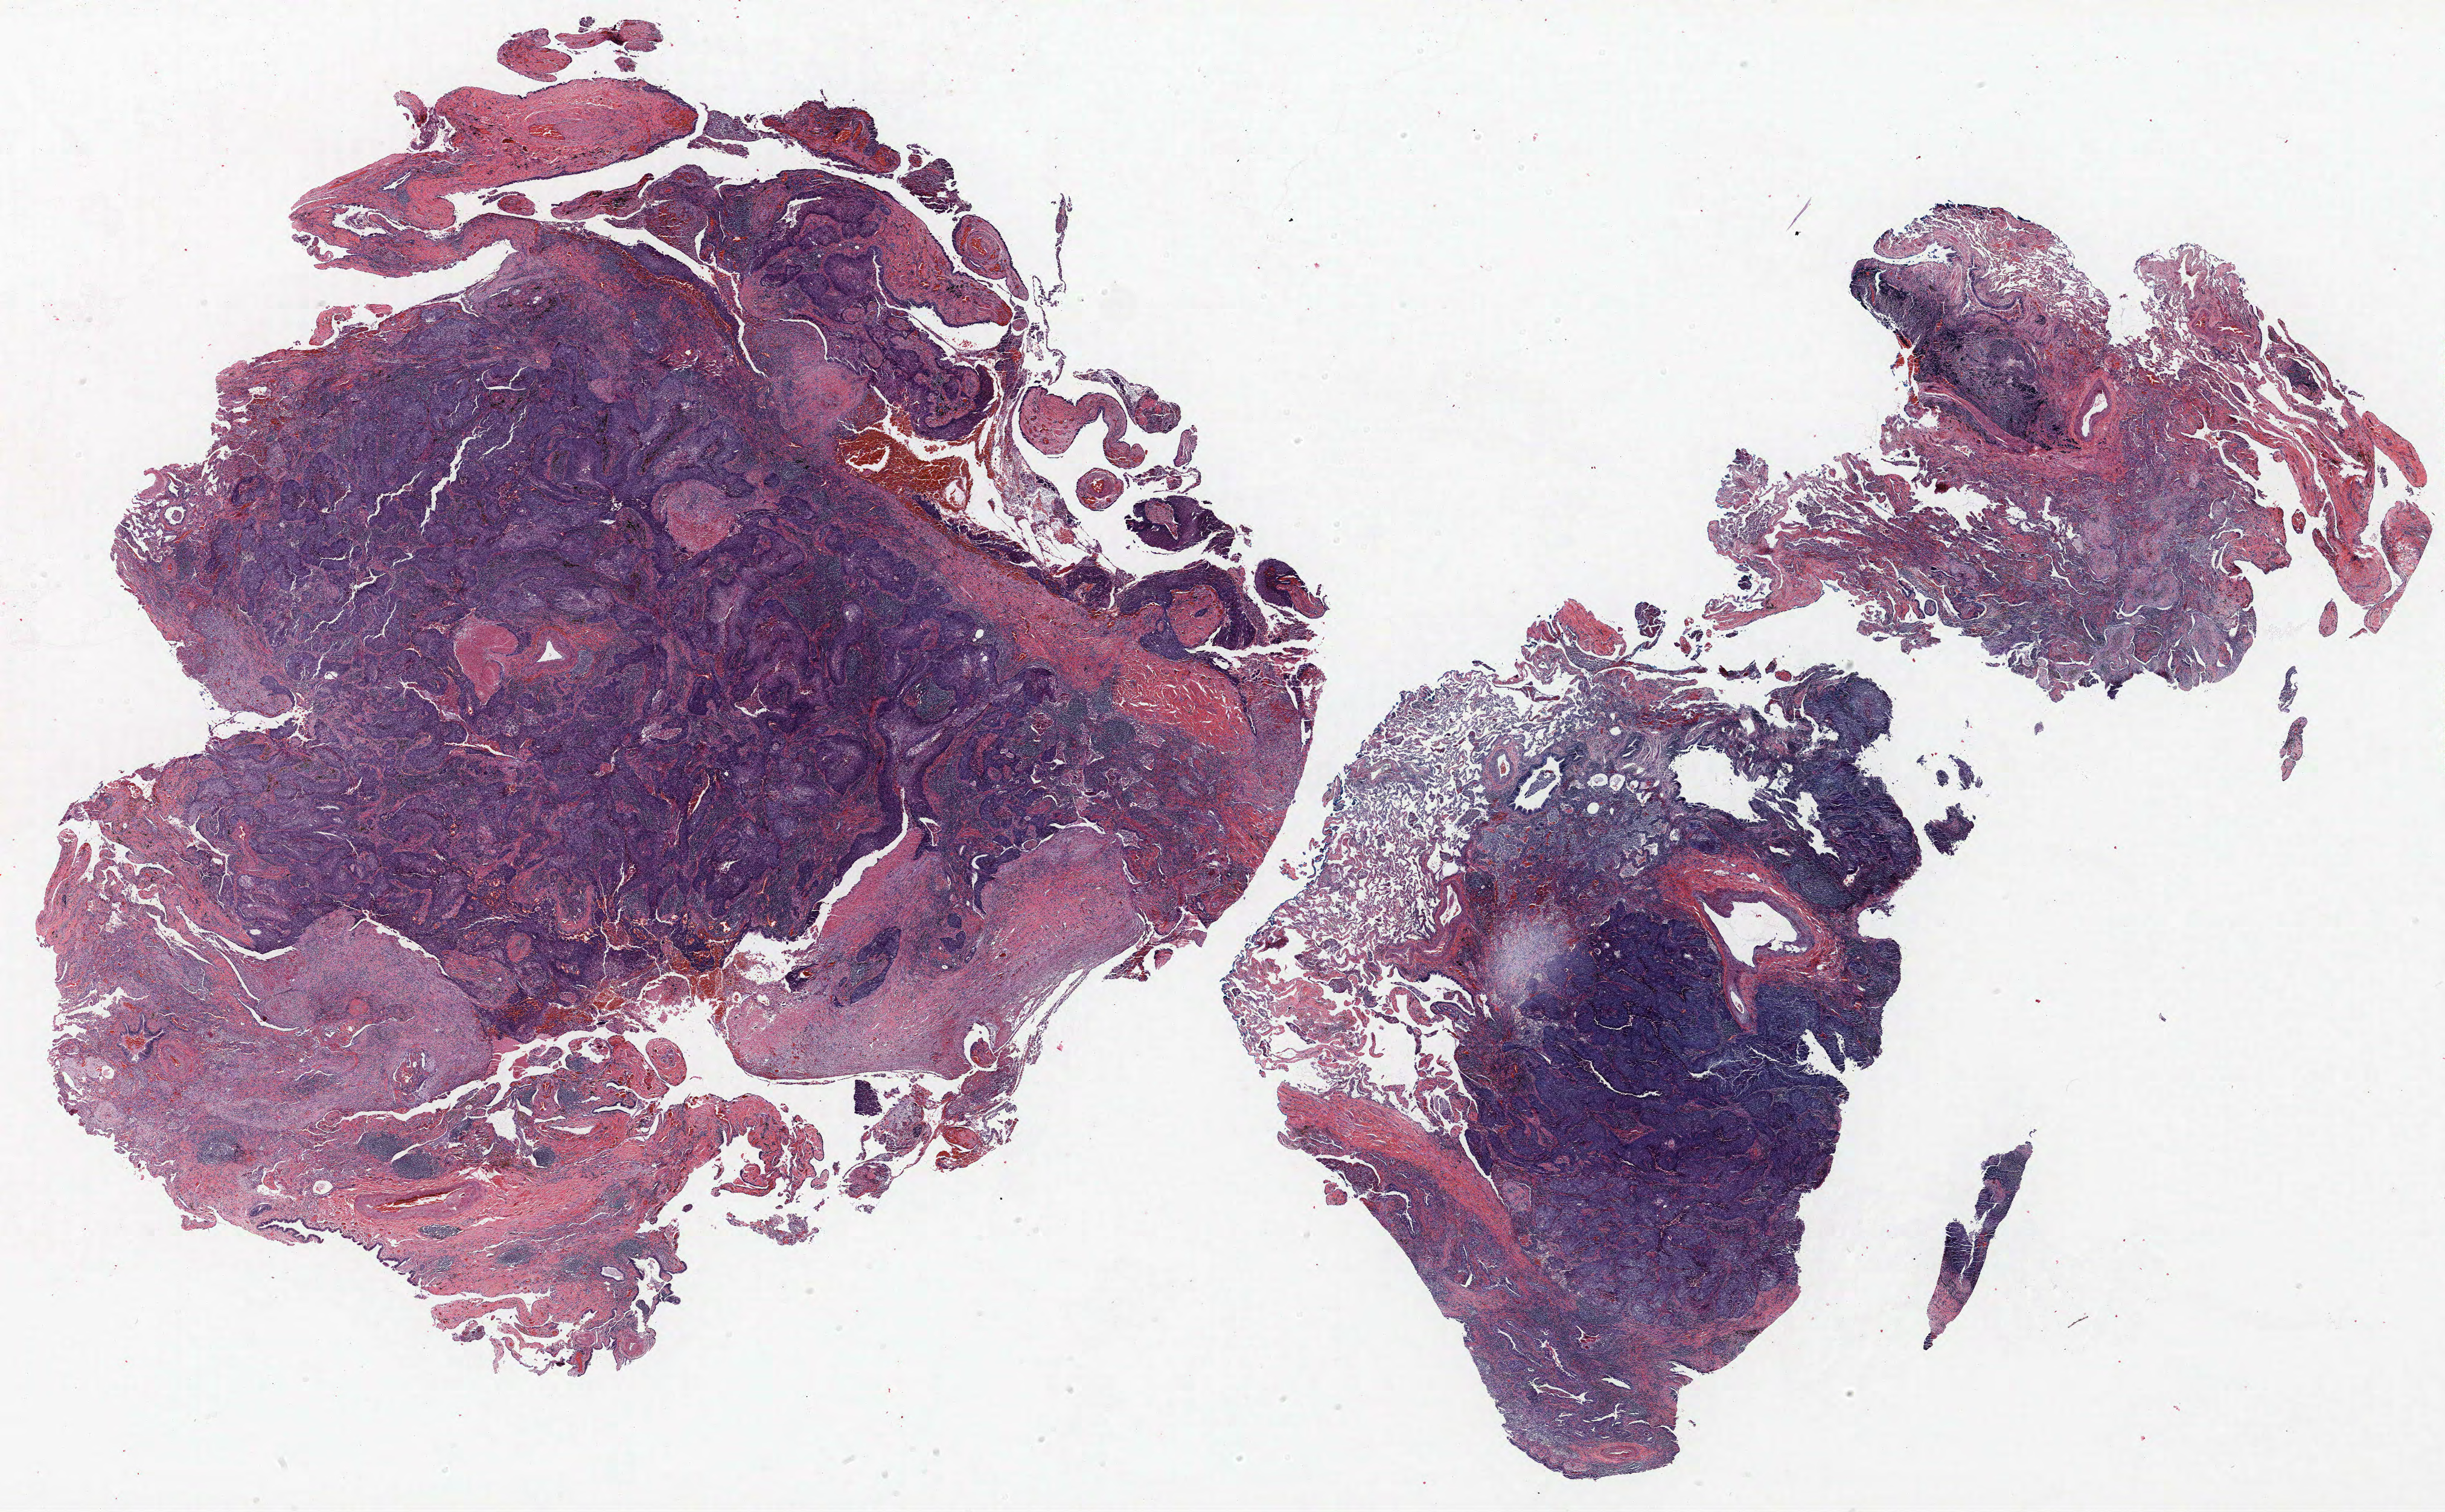
Hematoxylin and eosin (H&E) stained whole-slide image — a low-resolution overview of the entire scanned area, about 32.4 x 20.0 mm (from a 40x scan); FFPE section; lung. Male, age 58 at enrolment. Current smoker at enrolment. Grade: moderately differentiated (G2).
Stage (AJCC 6th edition): IB. Participant's lung-cancer diagnosis: Squamous cell carcinoma, keratinizing, NOS. Primary tumour location (clinical record): right lower lobe. Tumour size (pathology): 38 mm. Note: participant had 2 primary lung cancers recorded; fields above describe the first.